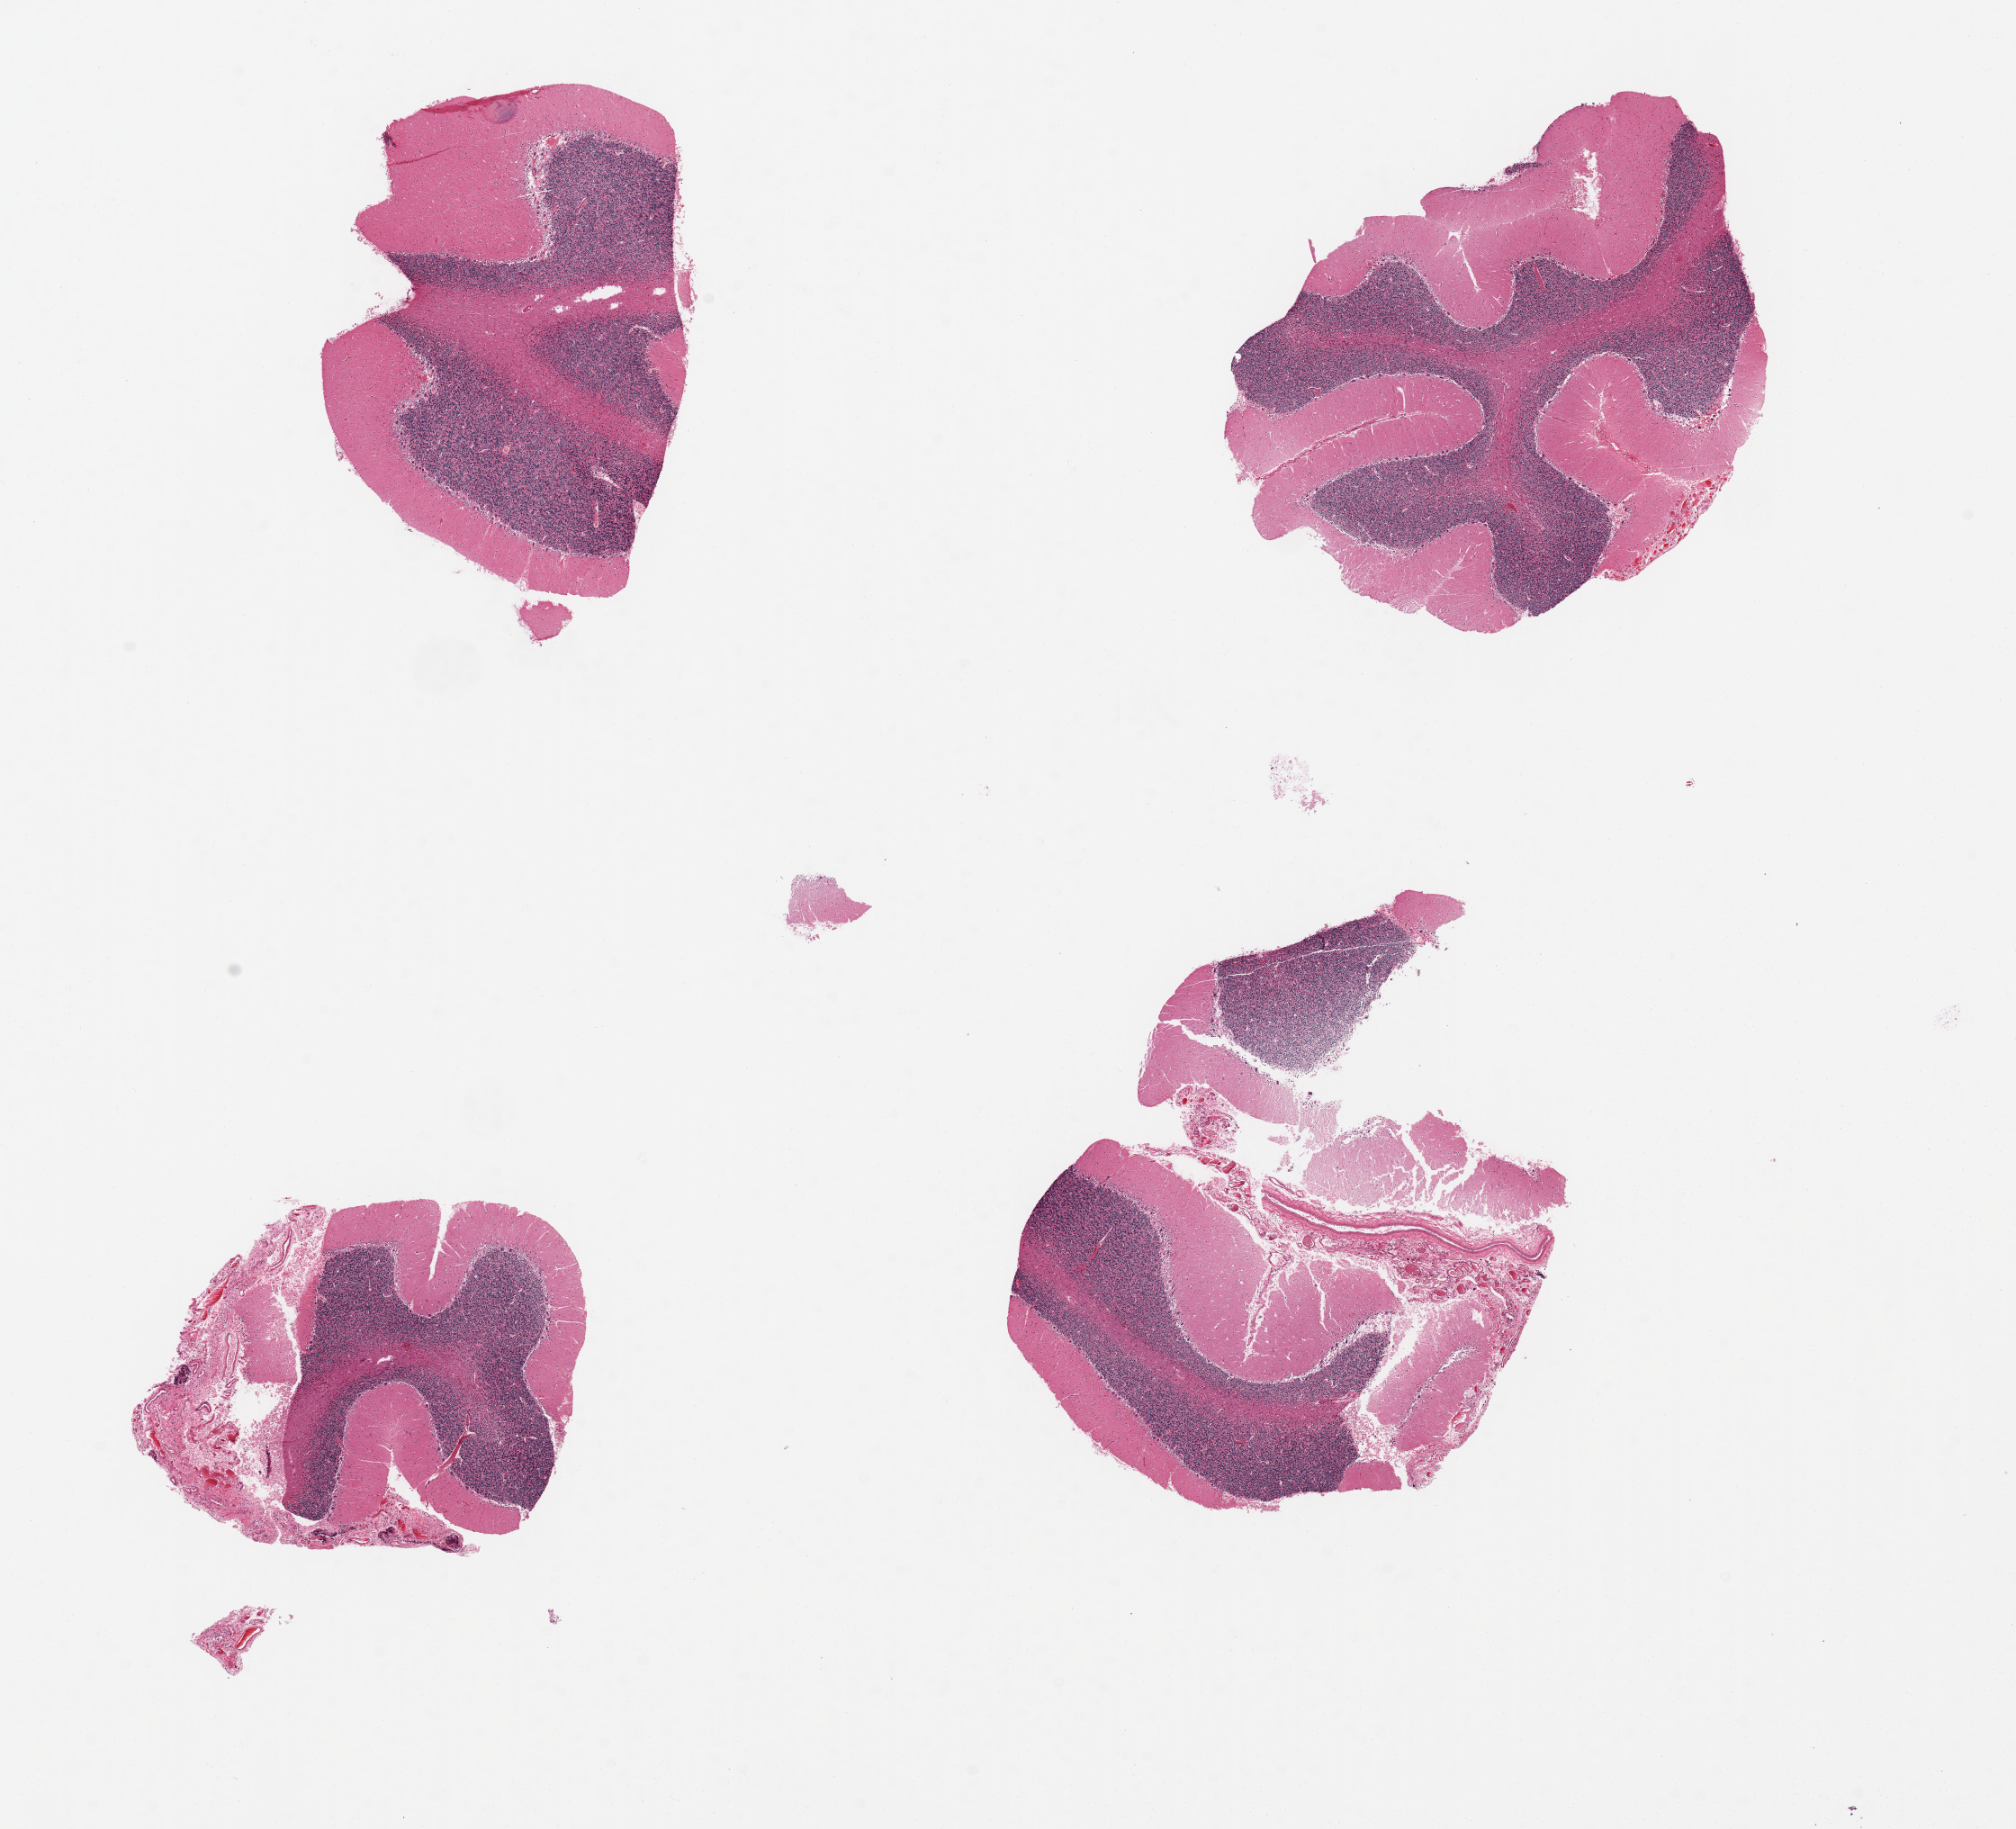
Whole-slide image, haematoxylin and eosin stain, whole scanned area (about 17.7 x 16.1 mm, slide scanned at 20x) shown as a low-resolution overview, PAXgene-fixed paraffin-embedded (PFPE) section, section of cerebellum (target tissue), tissue donor sample.
Review note (as recorded): 4 pieces up to 4x4 mm; 2 pieces have meninges attached.